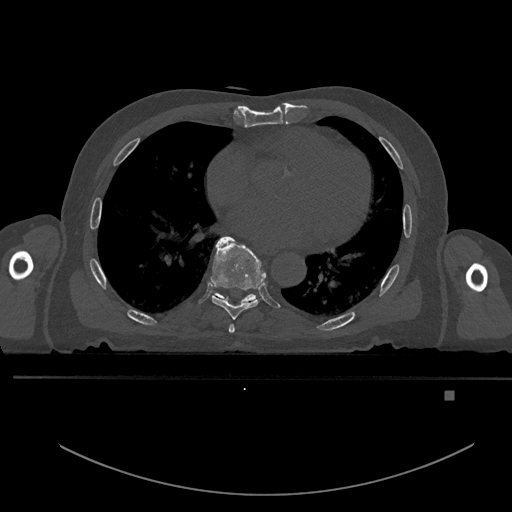
CT including the spine, one axial slice. Slice 241 of 969 in the series (ordered by position). Bone window (W 1800 / L 400 HU). 0.5 mm slice thickness. 512 × 512 image matrix. Patient: male, 82 years. Case-level facts recorded for this patient, not image findings: primary cancer: prostate; vertebrae with lytic lesions (as recorded): T11, T9, T8, T2.
Outlined on this slice (semi-automatically segmented with operator editing):
- T6 vertebra: box from (x=229, y=324) to (x=235, y=333) px
- T7 vertebra: (x=211, y=236)–(x=266, y=320)
- T8 vertebra: (x=211, y=292)–(x=257, y=304)